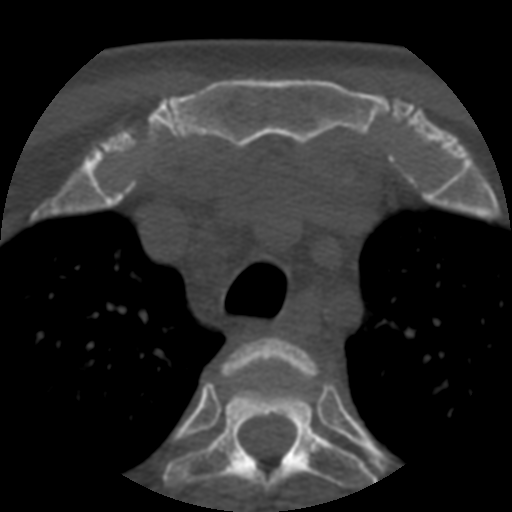
CT including the spine, one axial slice. Position 418 of 508 along the scan axis. Reconstruction kernel STANDARD. 120 kVp. Bone window (W 1800 / L 400 HU). 1.25 mm slice thickness. 512 × 512 image matrix, field of view 160 × 160 mm. Patient age 57 years. From the clinical record (not read from this slice): primary cancer: prostate.
Annotated regions visible in this slice (semi-automatically segmented with operator editing):
- T2 vertebra: bounding box <222,337,318,388> (left, top, right, bottom; pixels)
- T3 vertebra: <164,359,377,491>